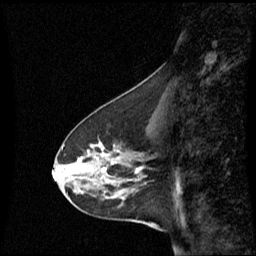
Breast MRI (dynamic contrast-enhanced), one sagittal slice; dynamic contrast-enhanced series, image 2 of 3 at this slice position (ordered by acquisition); 1.5 T; TE 4.2 ms, TR 8.4 ms; 2.2 mm slice thickness; 256 × 256 image matrix, field of view 240 × 240 mm. Patient: female, 45 years. Case-level facts recorded for this patient, not image findings: setting: breast cancer imaged before/during neoadjuvant chemotherapy; receptor status: HR-positive, HER2-negative.
Outlined on this slice (semi-automatically segmented with operator editing):
- analysis volume of interest (the breast-tissue region the enhancement analysis was run in; not a lesion): bounding box [x1, y1, x2, y2] px = [60, 126, 149, 215]
- tumour enhancement mask (voxels above the 70 % enhancement threshold inside the analysis volume of interest): [78, 150, 138, 173]